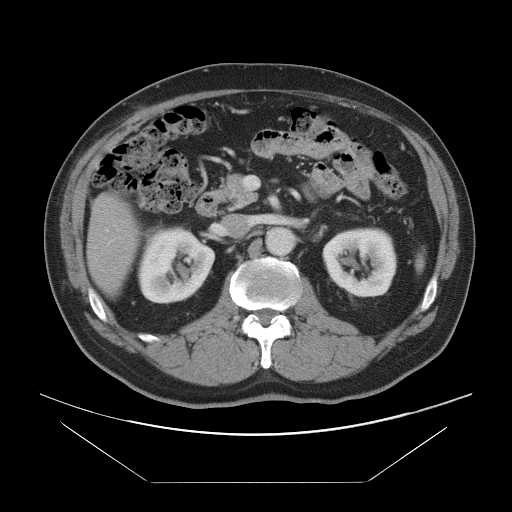
Contrast-enhanced abdominal CT, one axial slice. Position 41 of 97 along the scan axis. 120 kVp. Intravenous contrast given. Soft-tissue window (W 400 / L 40 HU). 5 mm slice thickness. 512 × 512 image matrix. Male patient, age 62 years. Case-level facts recorded for this patient, not image findings: diagnosis: colorectal cancer liver metastases, imaged before liver resection; multiple liver metastases: no; largest metastasis: 7 cm; disease in both lobes: yes.
Structures marked on this image (manually delineated by an expert):
- hepatic veins: bounding box <106,229,109,232> (left, top, right, bottom; pixels)
- liver: <89,195,136,295>
- planned liver remnant (the part of the liver to remain after resection): <89,195,136,293>
- portal vein (with intrahepatic branches): <108,241,111,245>